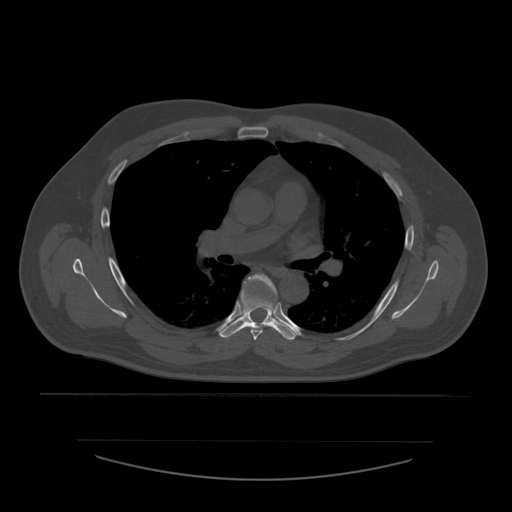
CT including the spine, one axial slice. Position 386 of 532 along the scan axis. Reconstruction kernel STANDARD. 120 kVp. Bone window (W 1800 / L 400 HU). 1.25 mm slice thickness. 512 × 512 image matrix. Patient age 44 years. From the clinical record (not read from this slice): primary cancer: soft tissue sarcoma.
Outlined on this slice (semi-automatic segmentation, software-assisted and operator-edited):
- T5 vertebra: bounding box <247,274,277,341> (left, top, right, bottom; pixels)
- T6 vertebra: <220,280,299,341>